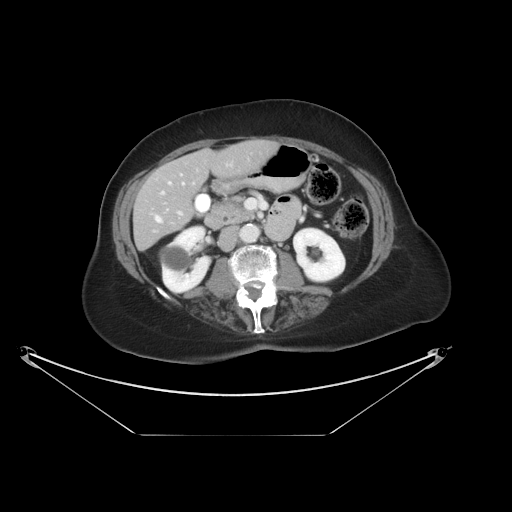
Contrast-enhanced abdominal CT, one axial slice. Slice 13 of 36 in the series (ordered by position). Reconstruction kernel STANDARD. Intravenous contrast given. Soft-tissue window (W 400 / L 40 HU). 5 mm slice thickness. 512 × 512 image matrix, field of view 500 × 500 mm. Female patient, age 70 years. From the clinical record (not read from this slice): diagnosis: colorectal cancer liver metastases, imaged before liver resection; multiple liver metastases: no; largest metastasis: 2.5 cm.
Annotated regions visible in this slice (outlined manually by an expert reader):
- hepatic veins: bounding box [x1, y1, x2, y2] px = [156, 182, 185, 222]
- liver: [134, 141, 275, 249]
- planned liver remnant (the part of the liver to remain after resection): [134, 141, 275, 249]
- portal vein (with intrahepatic branches): [162, 191, 182, 215]